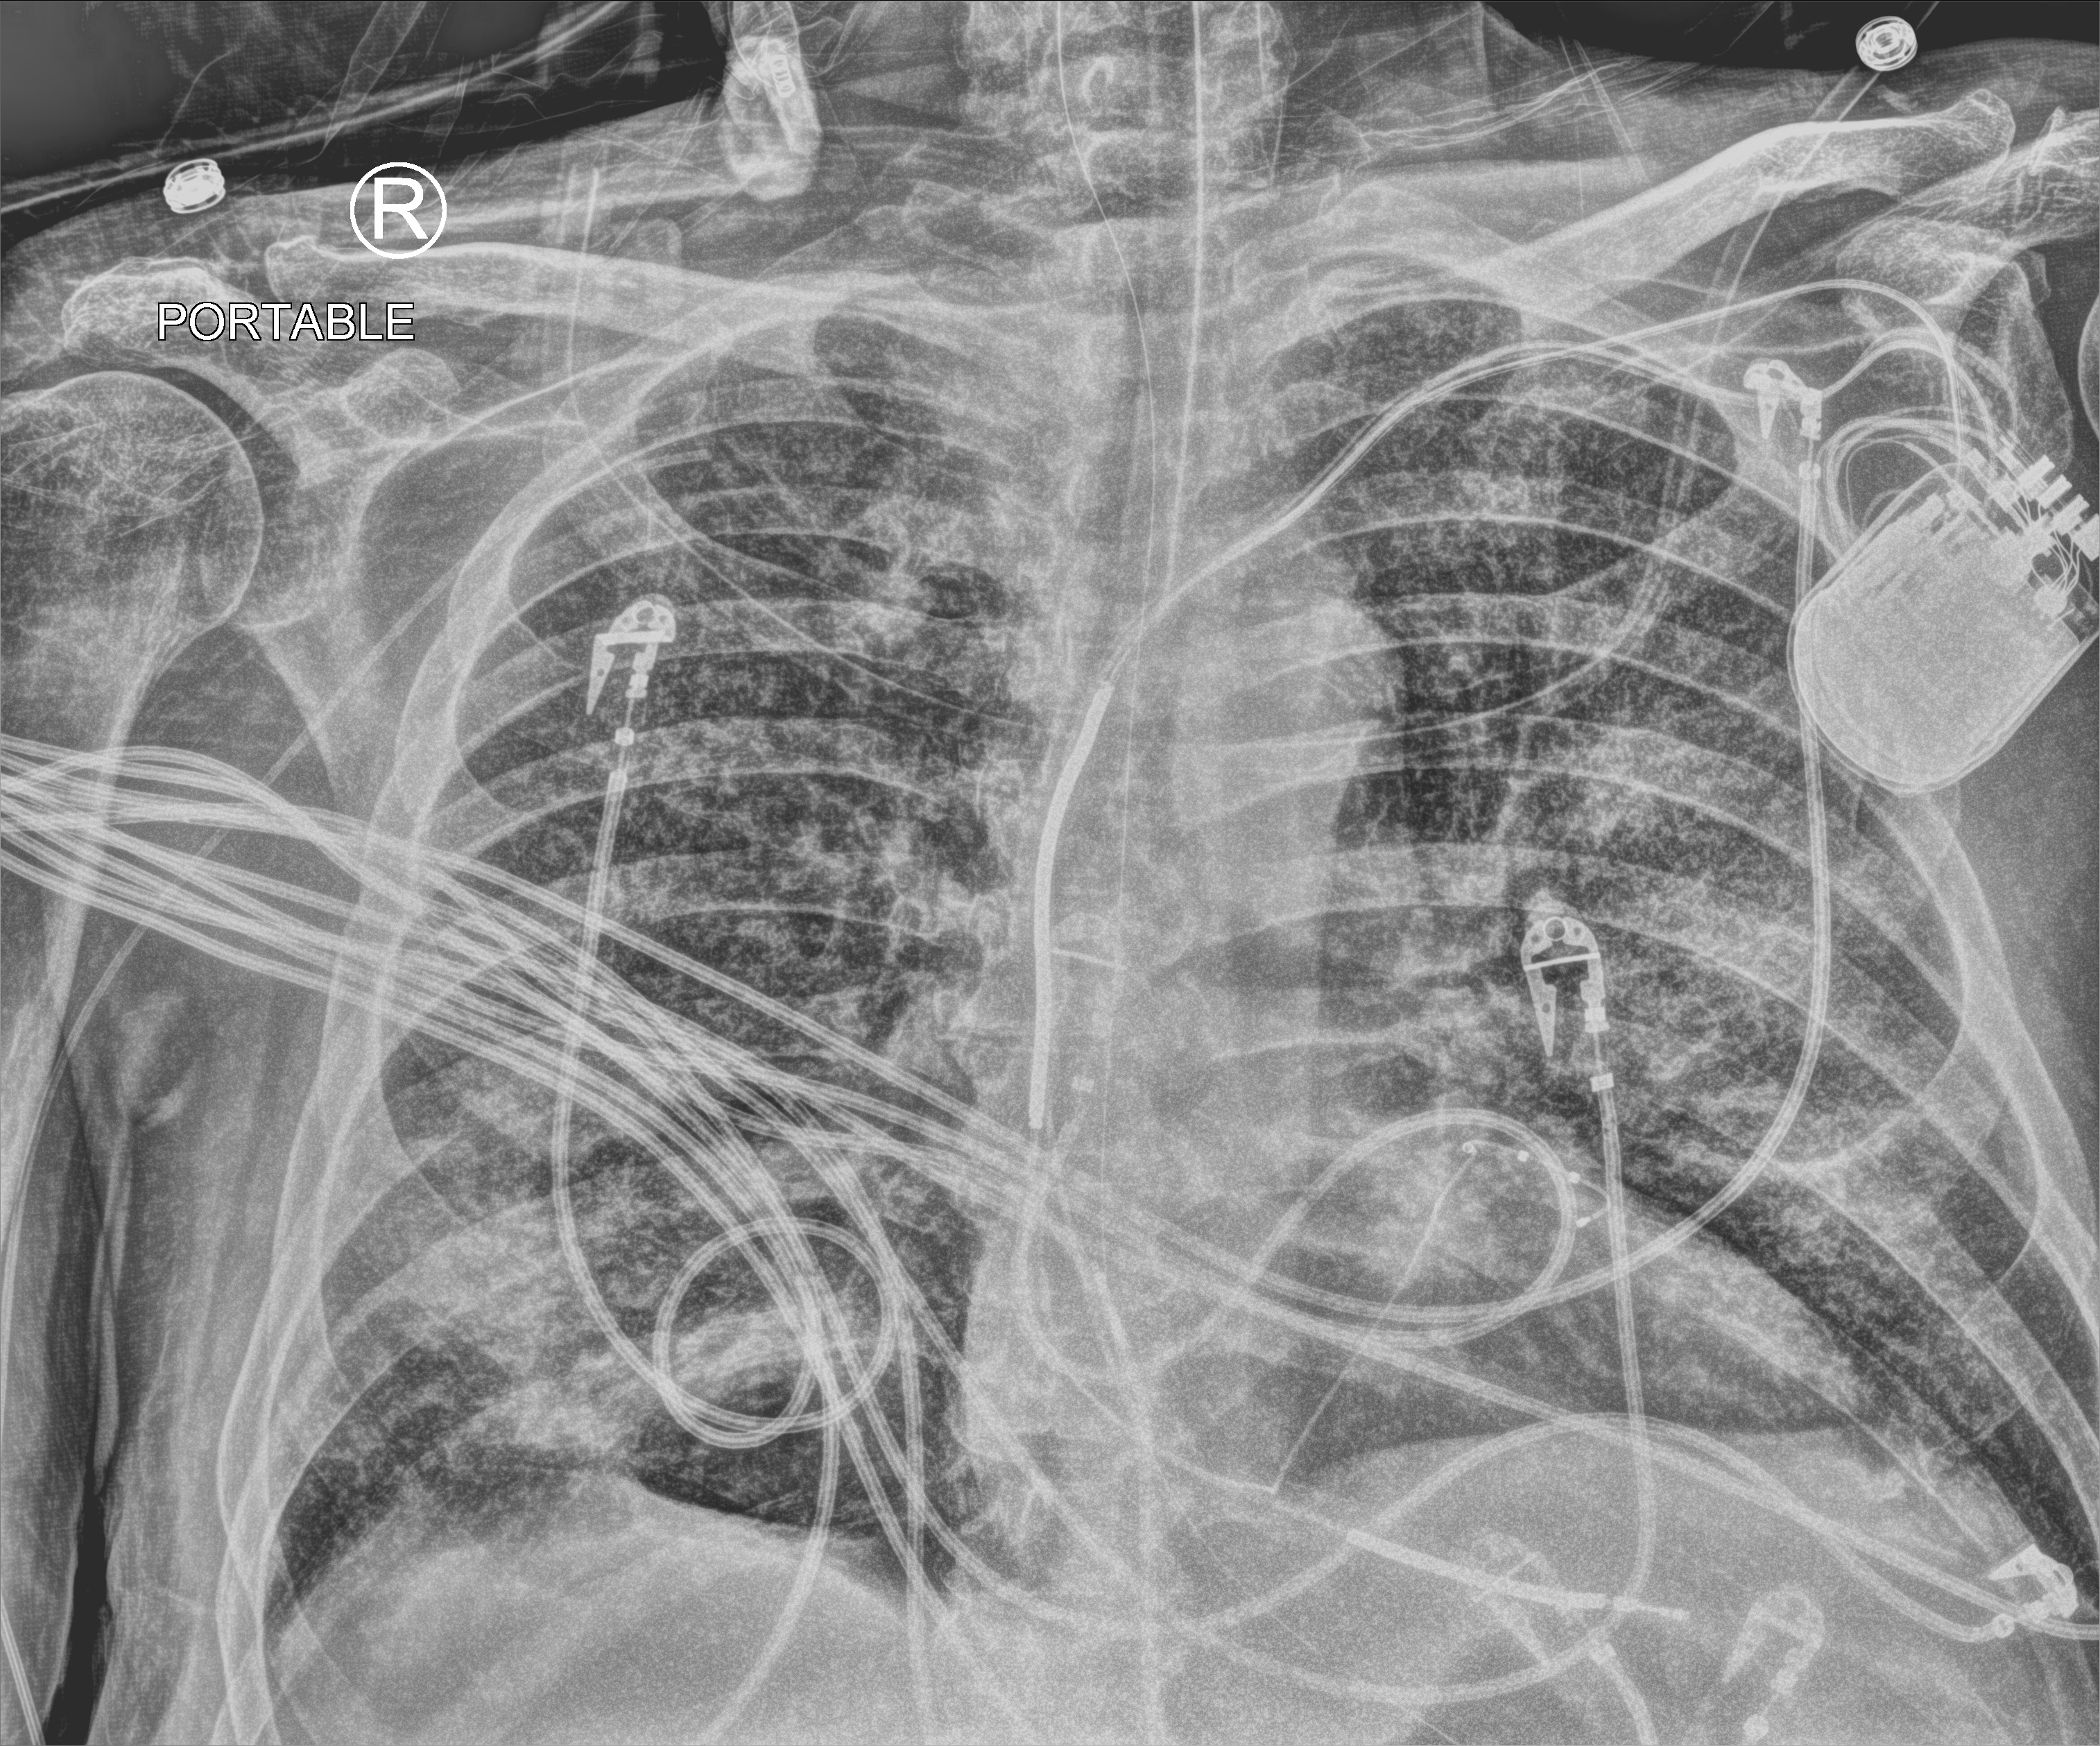
Chest X-ray (portable), anteroposterior (AP) projection. Patient hospitalised with COVID-19; male, aged 60–74 years.
Hospital-stay facts (about this admission, not read from this image; timing relative to this image not recorded):
- mechanically ventilated during this hospital stay: yes
- hypertension (admission record): yes
- length of hospital stay: 36 days